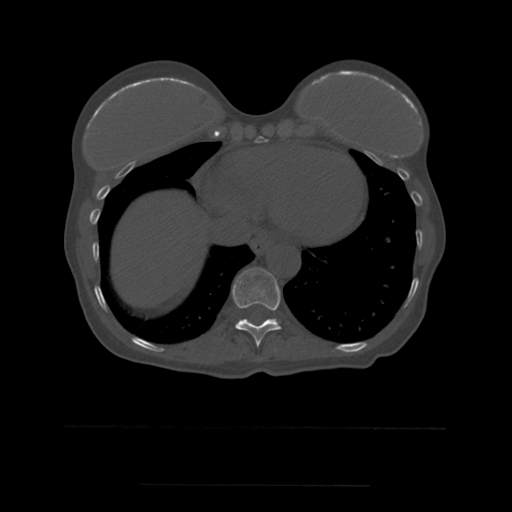
CT including the spine, one axial slice; slice 299 of 544 in the series (ordered by position); bone window (W 1800 / L 400 HU); 1.25 mm slice thickness; 512 × 512 image matrix, field of view 350 × 350 mm. Patient age 58 years. Case-level facts recorded for this patient, not image findings: primary cancer: lung.
Annotated regions visible in this slice (semi-automatically segmented with operator editing):
- T10 vertebra: box from (x=232, y=268) to (x=282, y=347) px
- T11 vertebra: (x=242, y=319)–(x=277, y=321)